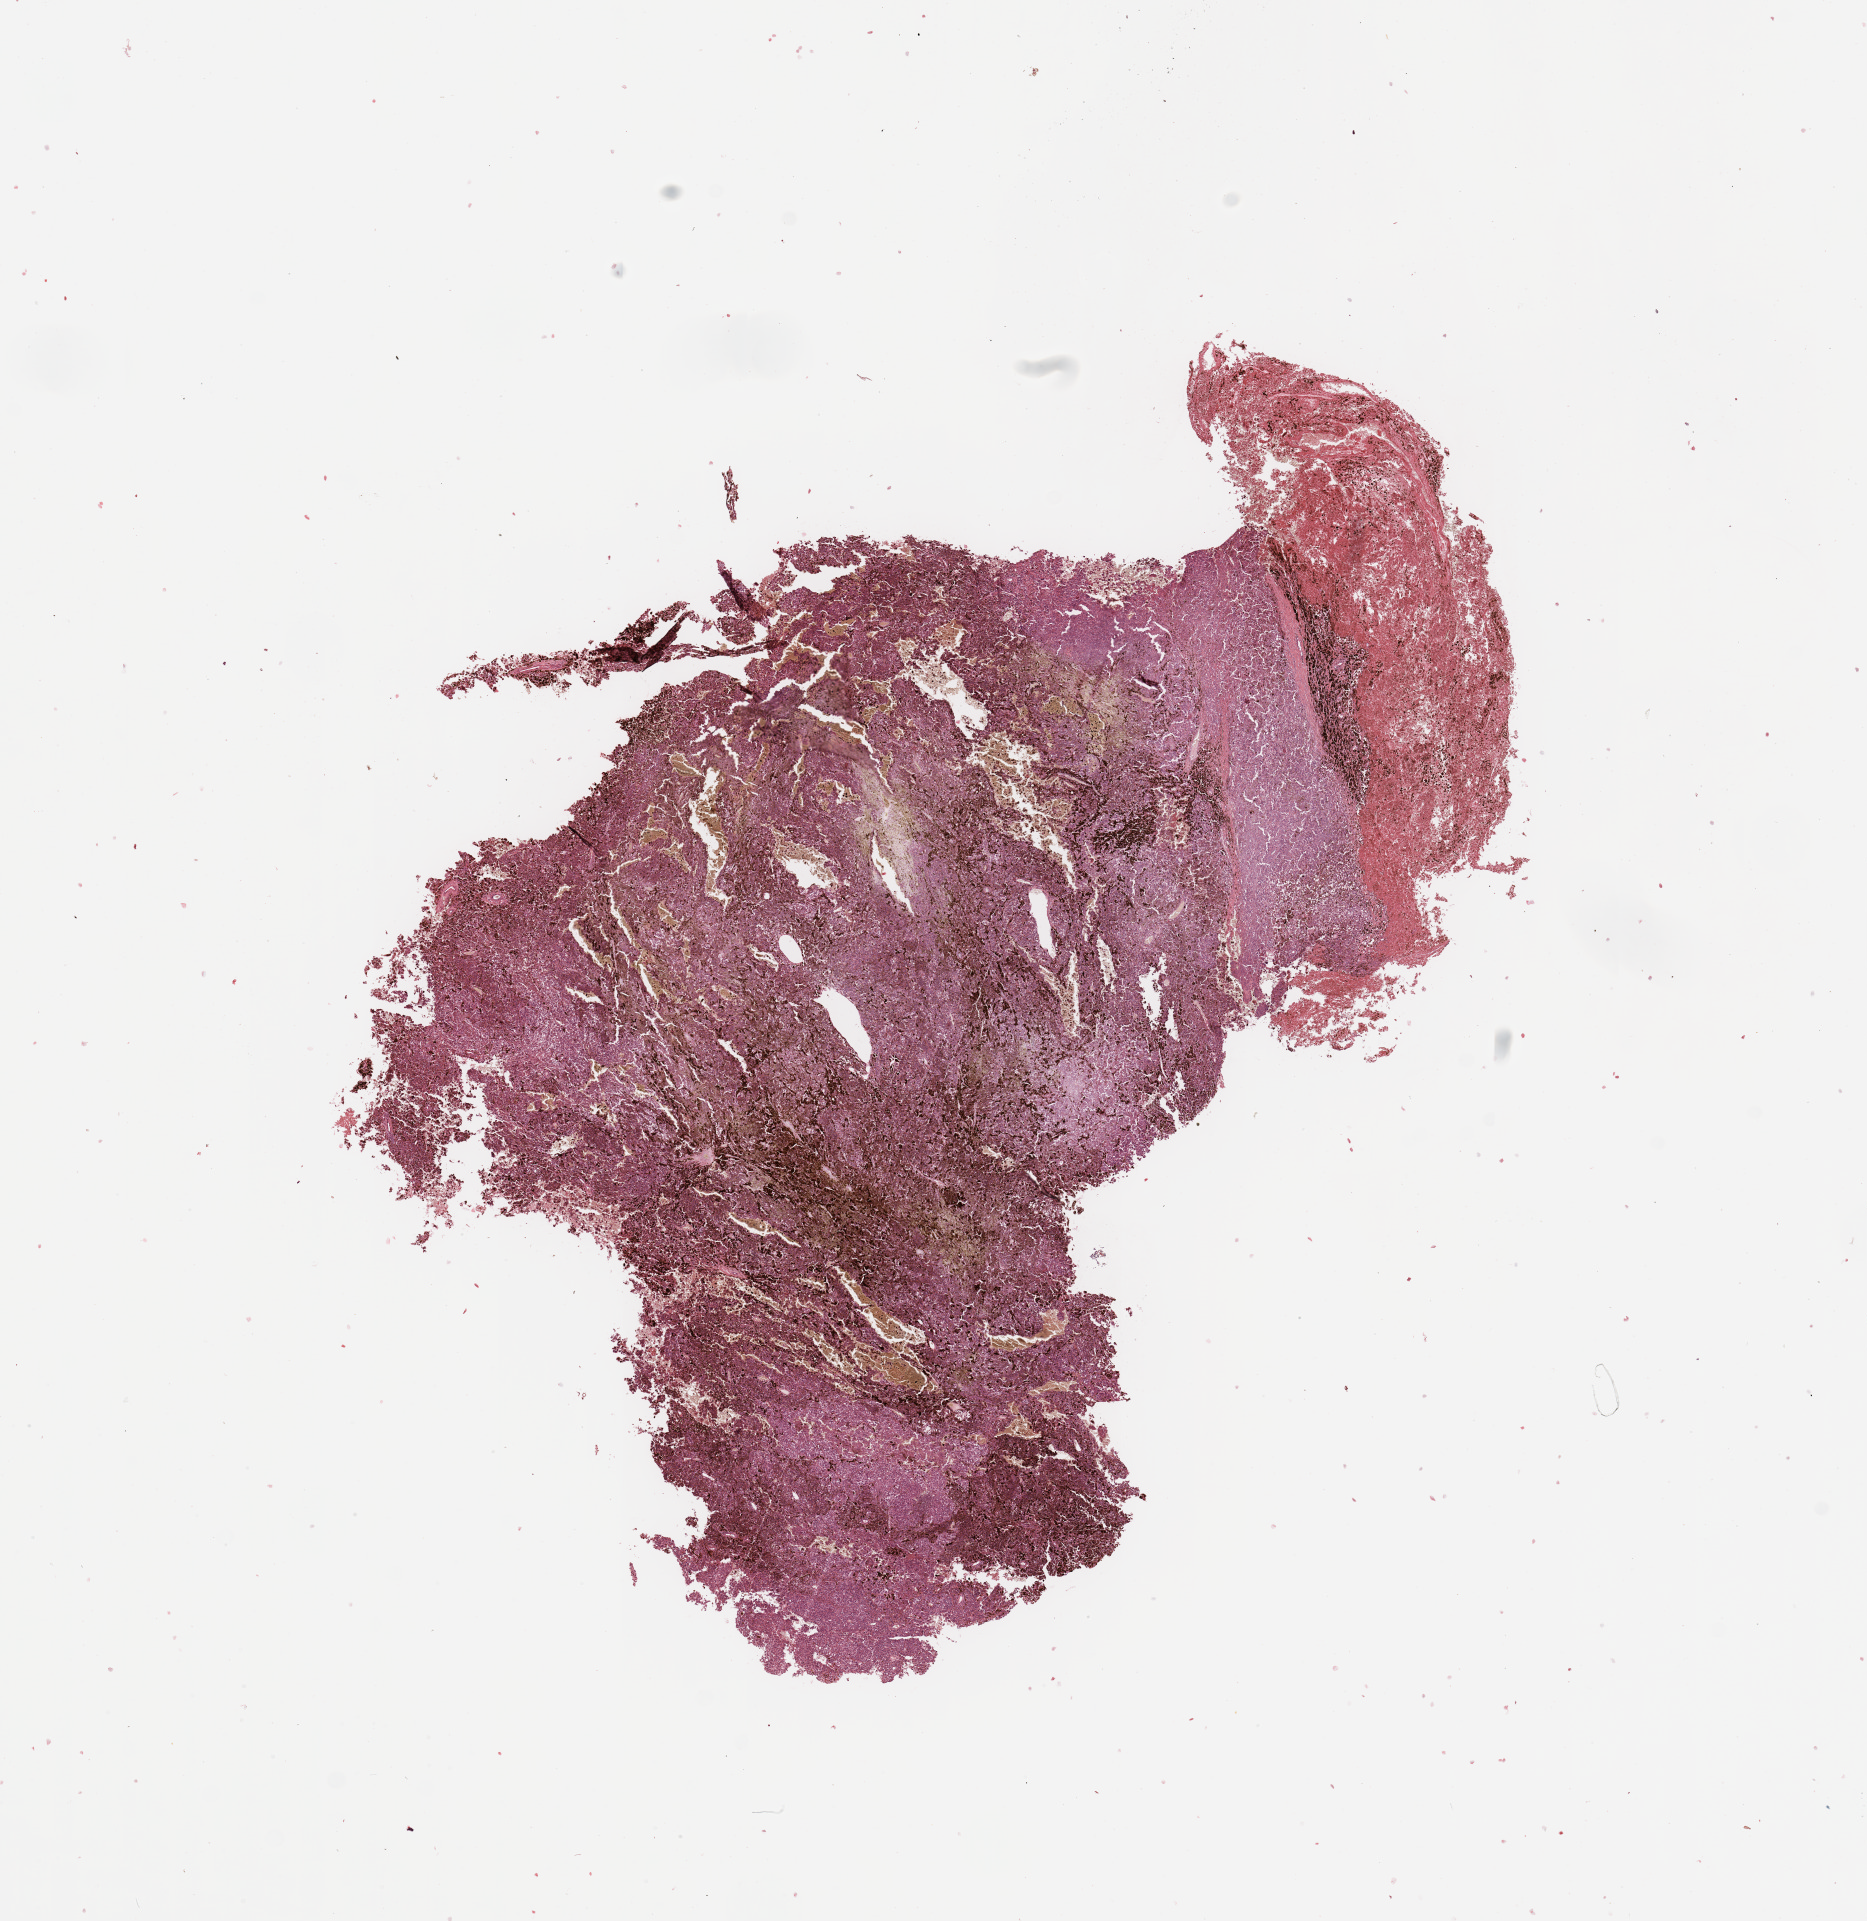
H&E-stained whole-slide image — a low-resolution overview of the entire scanned area, about 14.8 x 15.2 mm. Tumour tissue sample, sampled site: lymph node. Patient: female, age 63 years. Pathologist review of this section (percent, as recorded): tumour nuclei 80%, necrosis 5%.
- this section: metastatic tumour tissue
- primary tumour site (as recorded): extremities
- patient diagnosis: Malignant melanoma, NOS